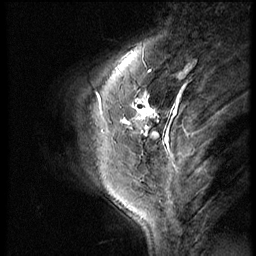
Breast MRI (dynamic contrast-enhanced), one sagittal slice; slice 16 of 56 in the series (ordered by position); 3 images stored at this slice position (order not interpretable as contrast timing); 1.5 T; TE 4.2 ms, TR 9 ms; 2.5 mm slice thickness; 256 × 256 image matrix, field of view 180 × 180 mm. Patient: female, 46 years. From the clinical record (not read from this slice): setting: breast cancer imaged before/during neoadjuvant chemotherapy; receptor status: HER2-positive.
Outlined on this slice (semi-automatically segmented with operator editing):
- analysis volume of interest (the breast-tissue region the enhancement analysis was run in; not a lesion): bounding box <73,86,164,161> (left, top, right, bottom; pixels)
- tumour enhancement mask (voxels above the 140 % enhancement threshold inside the analysis volume of interest): <123,99,158,135>